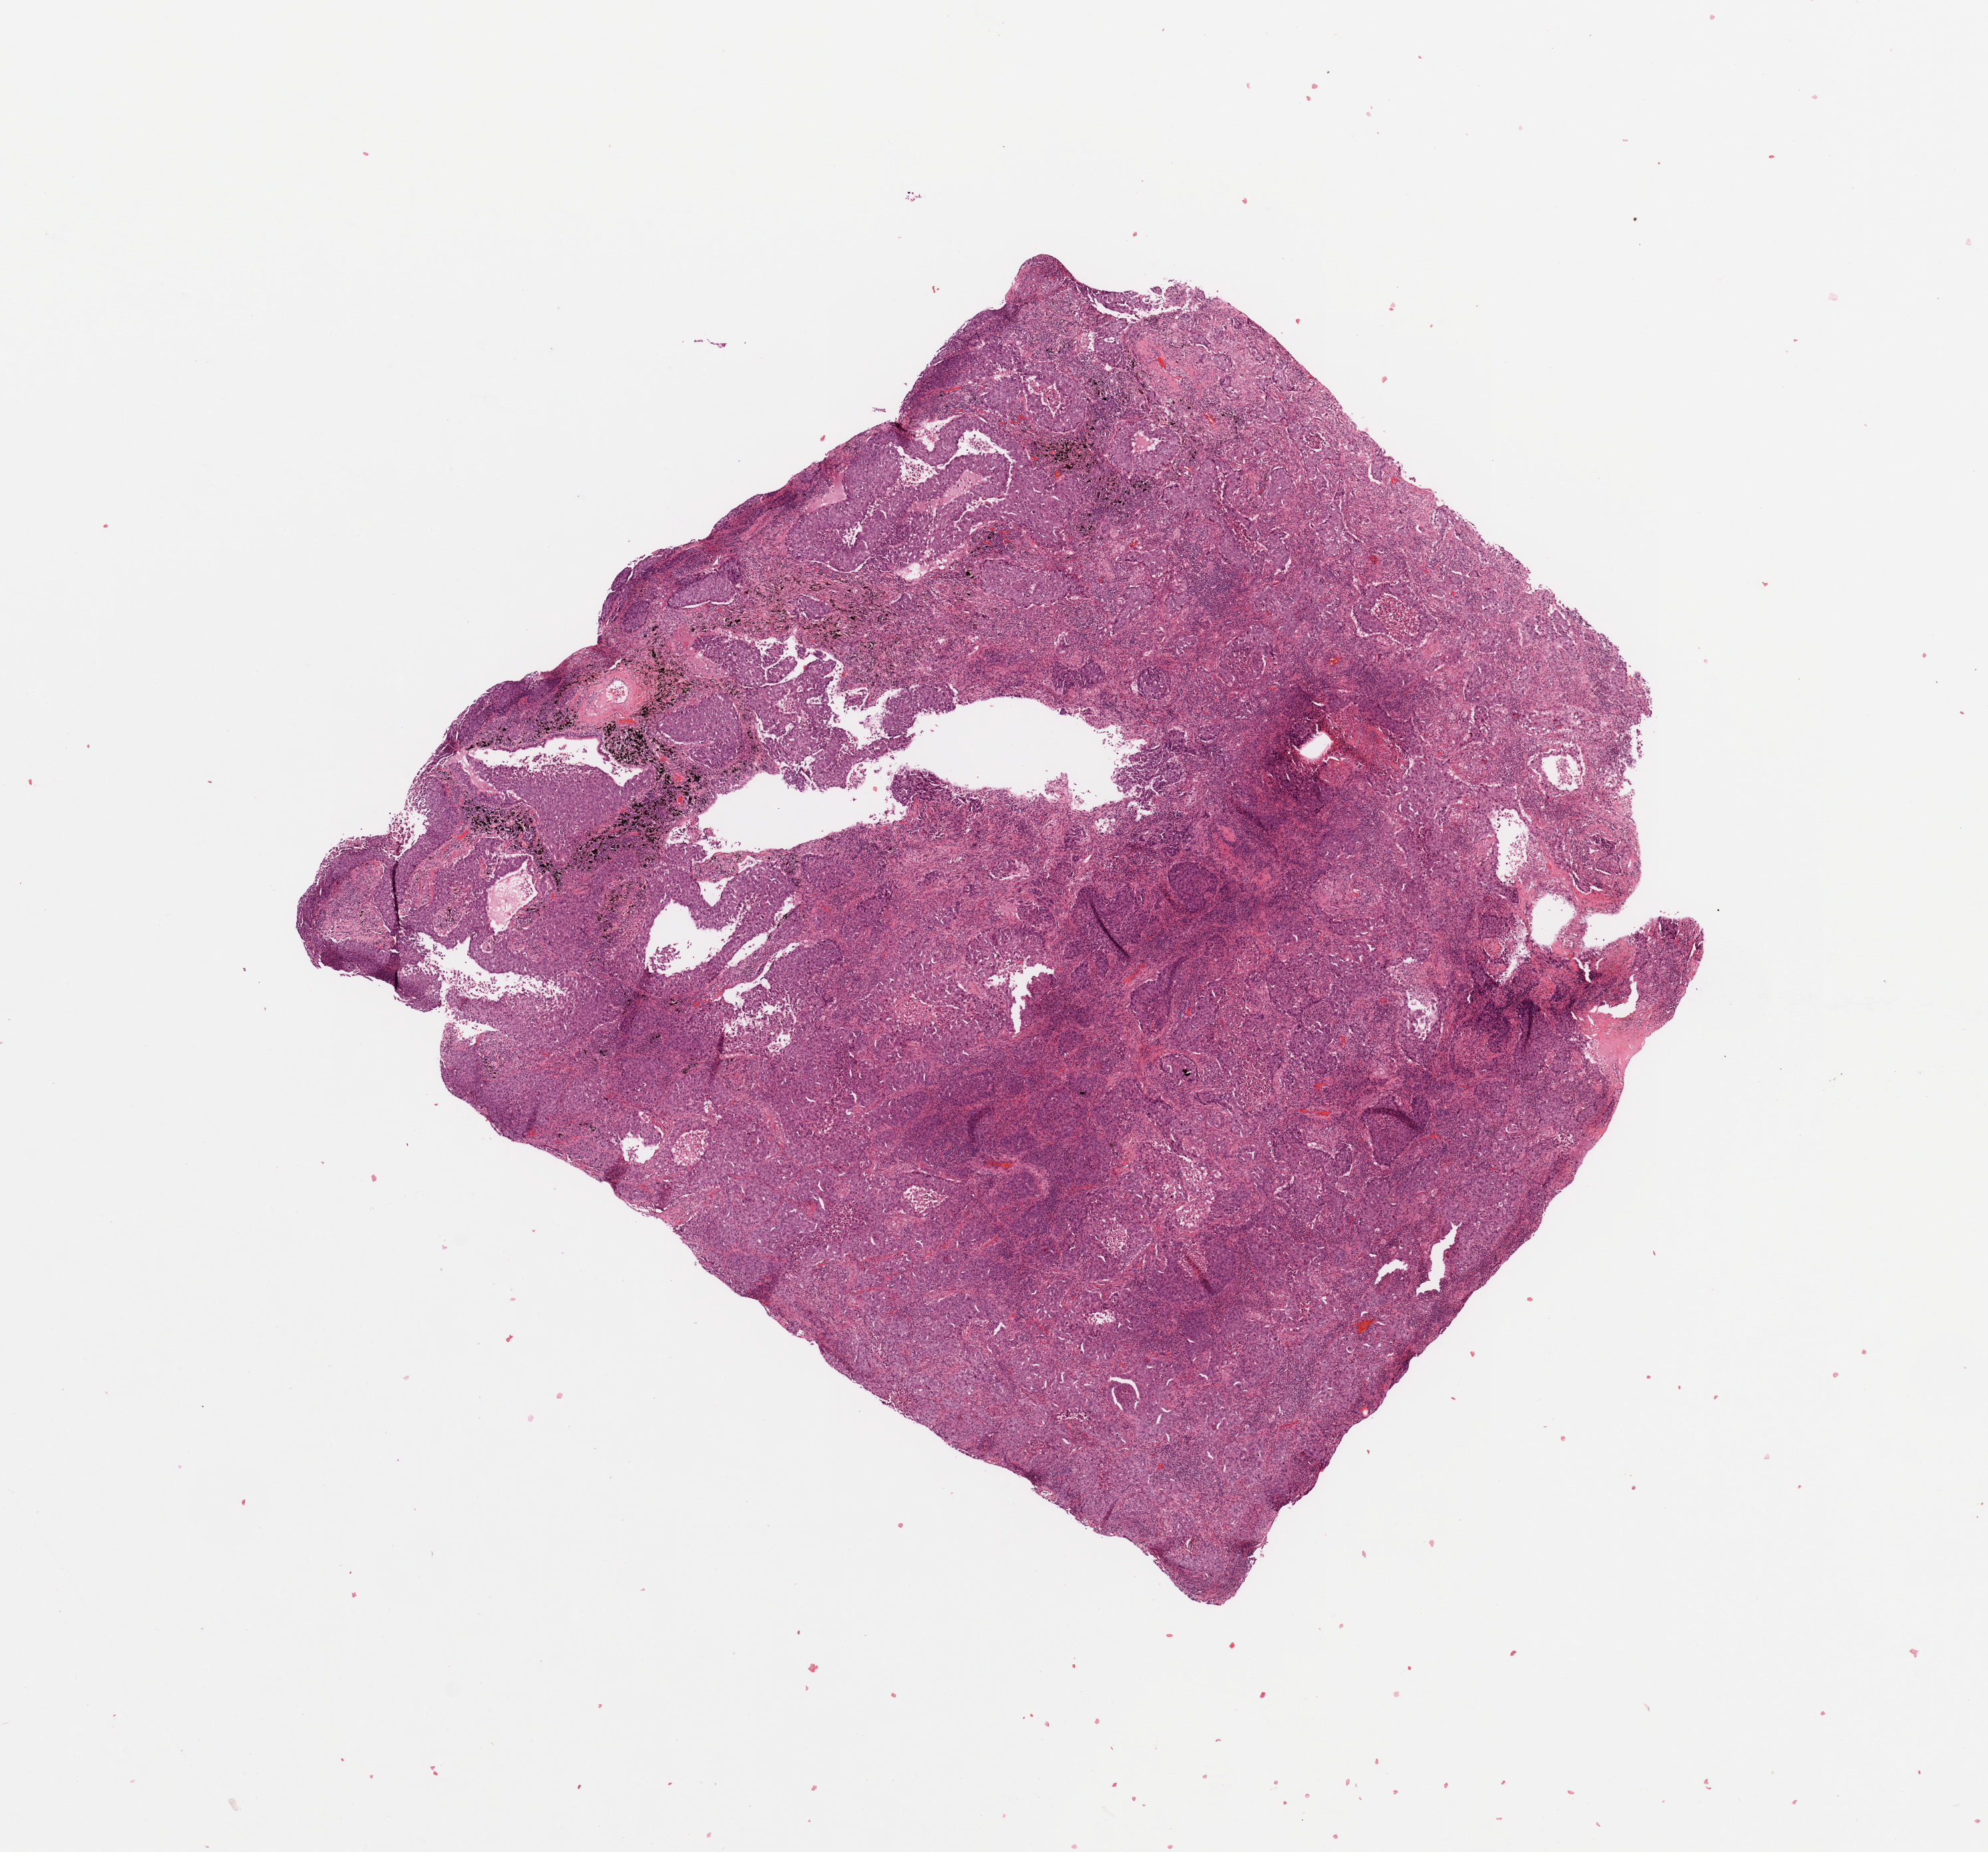
Hematoxylin and eosin (H&E) stained whole-slide image — whole scanned area (about 11.8 x 11.0 mm, from a 20x scan) shown as a low-resolution overview, tumour tissue sample, sampled site: lung. 72-year-old male patient.
Histologic diagnosis: Adenocarcinoma, NOS.